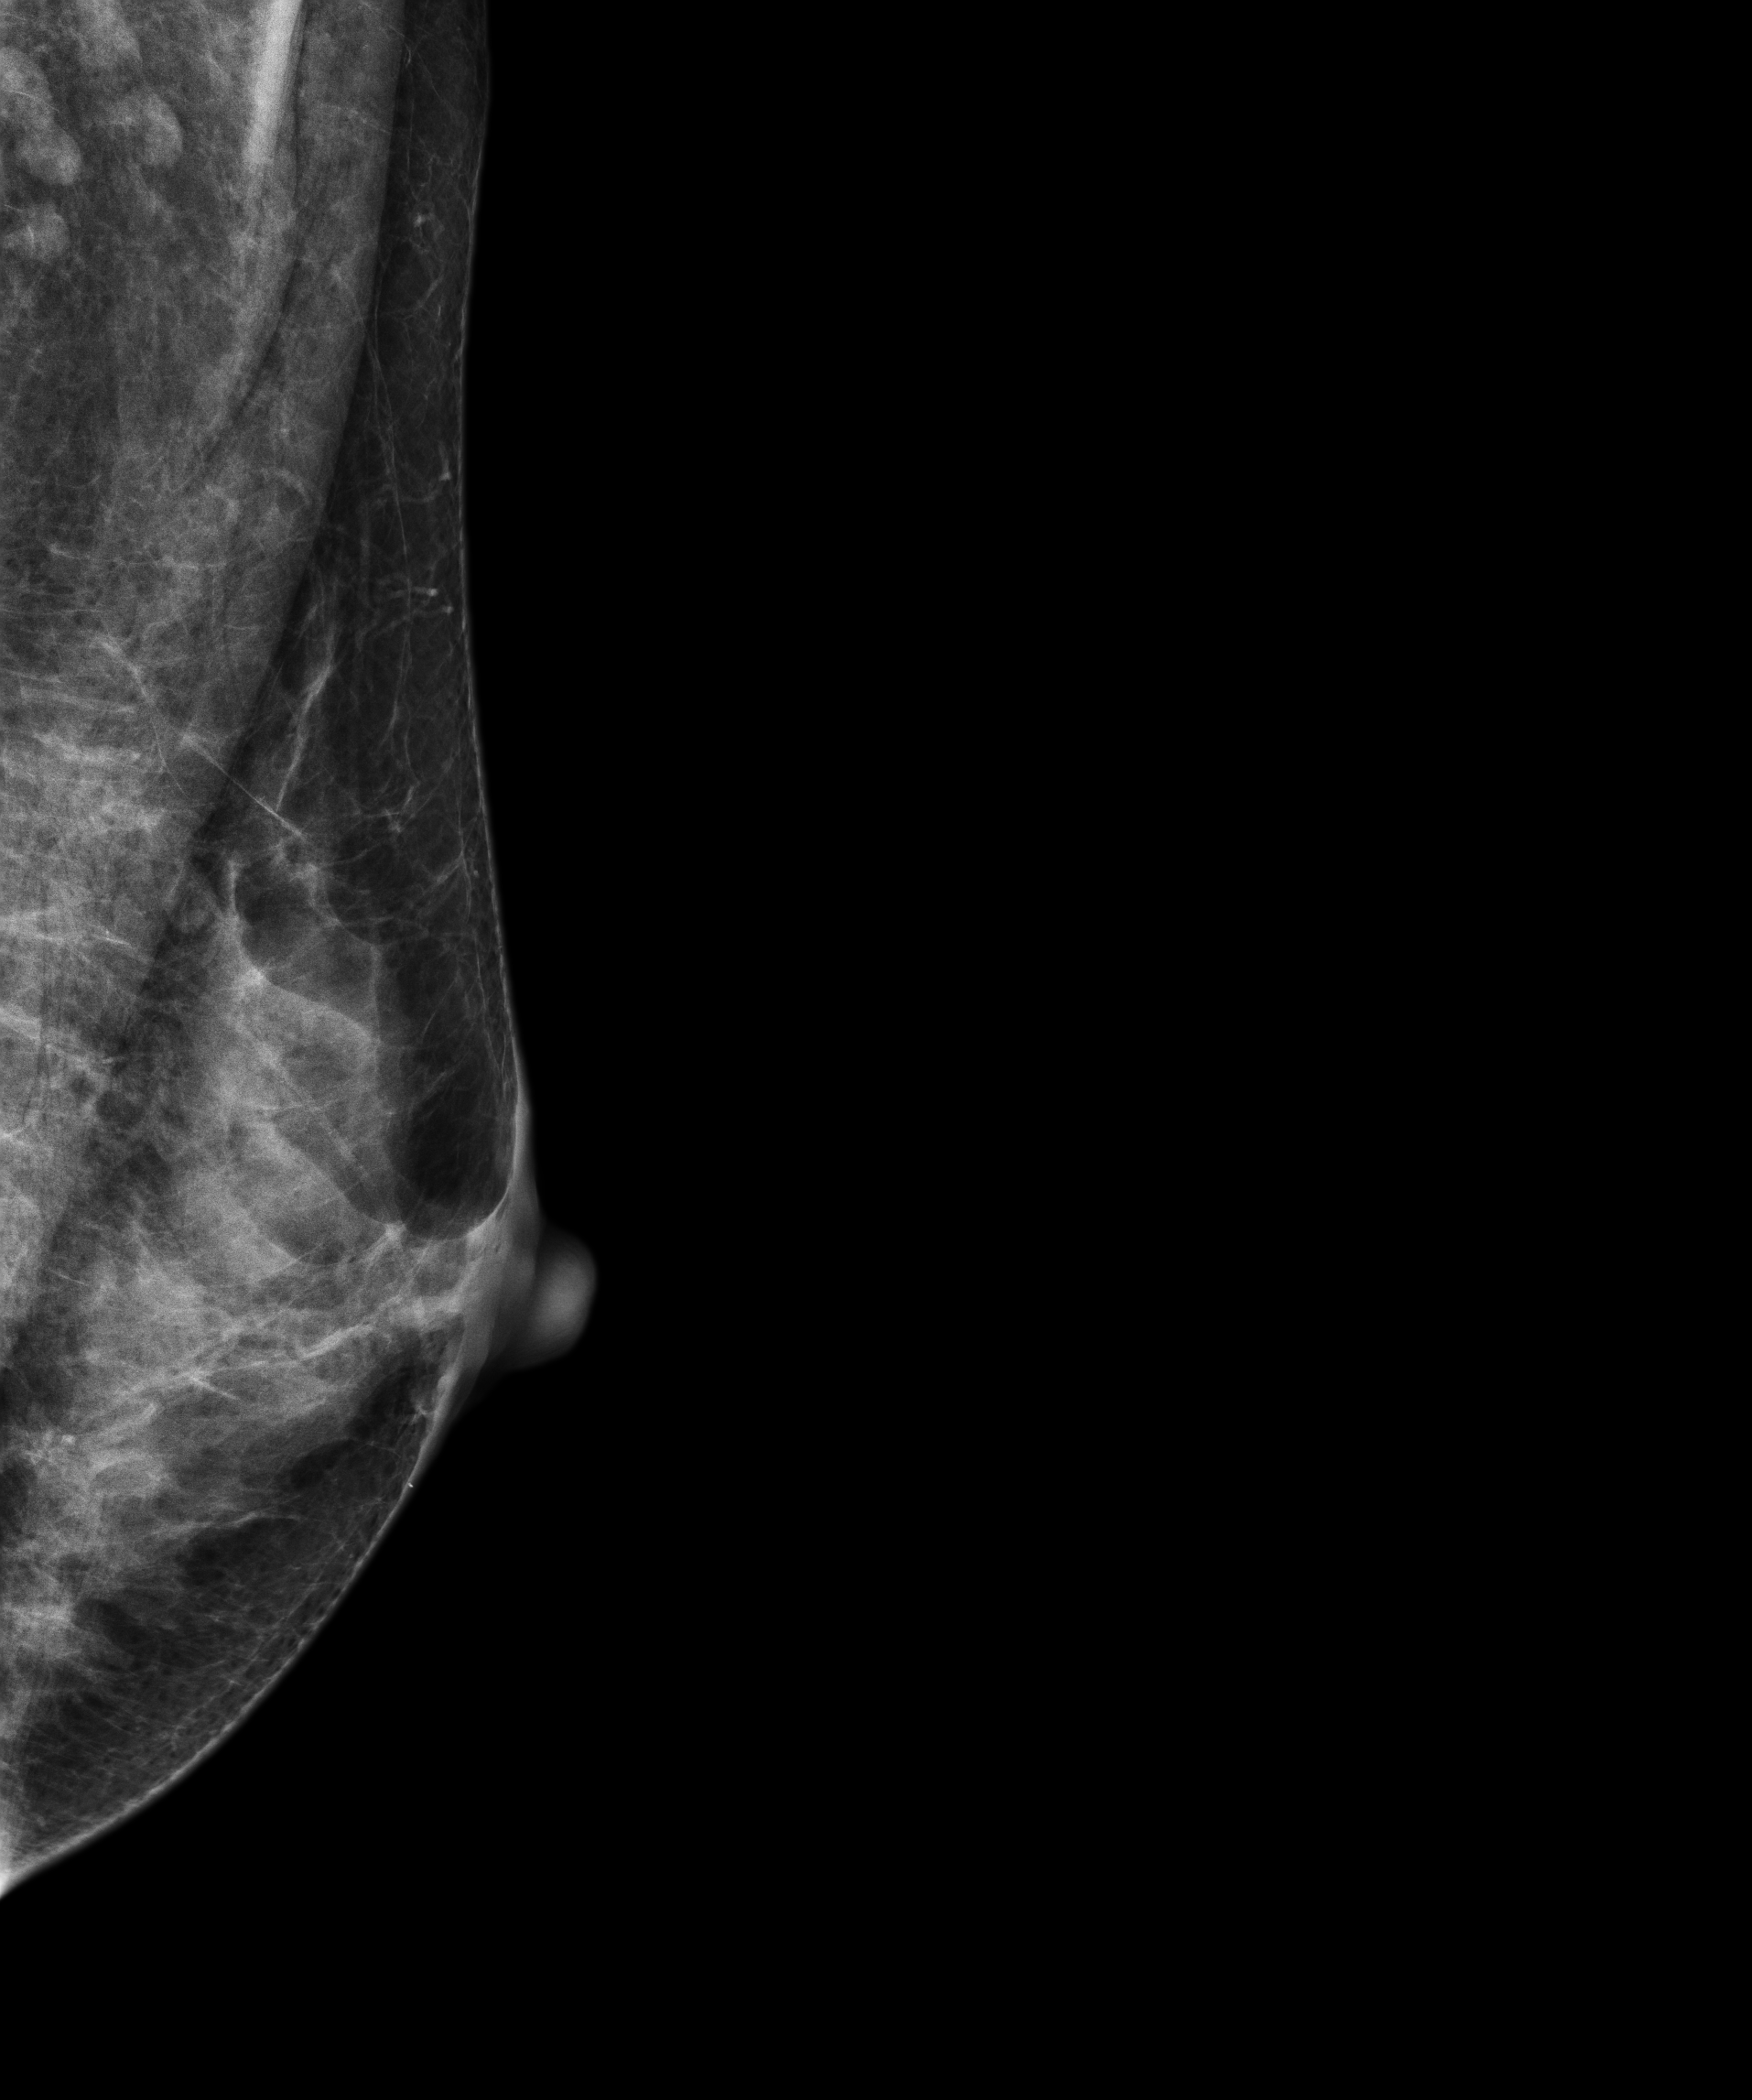
Screening examination; system: Senographe Essential ADS_56.21.3. Patient: female, 46 years.
Image type: full-field digital mammogram. Breast: left. Projection: mediolateral oblique (MLO) view. Breast density at the screening exam (both breasts): extremely dense (BI-RADS density category d). Final BI-RADS category for the screening round (tomosynthesis exam, both breasts): category 1. Recall: no recall after this screen.